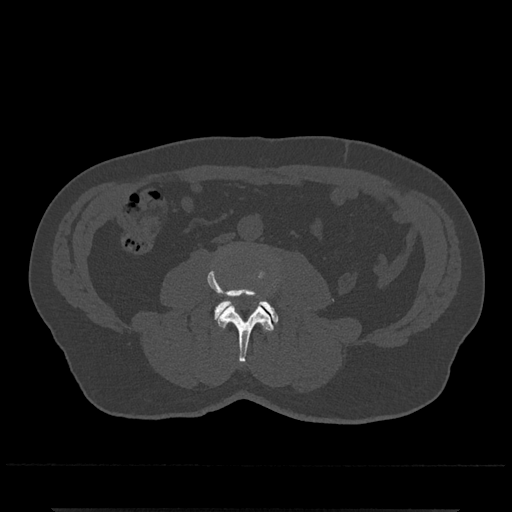
CT including the spine, one axial slice. Slice 201 of 797 in the series (ordered by position). Reconstruction kernel Br40s/3. 120 kVp. Bone window (W 1800 / L 400 HU). 512 × 512 image matrix, field of view 393 × 393 mm. Patient: male, 67 years. From the clinical record (not read from this slice): primary cancer: prostate.
Outlined on this slice (semi-automatically segmented with operator editing):
- L3 vertebra: bounding box (x1, y1, x2, y2) in pixels: (208, 268, 278, 363)
- L4 vertebra: (214, 299, 279, 325)